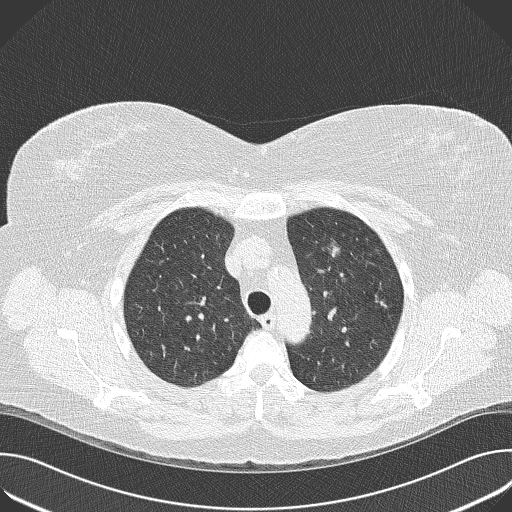
Low-dose screening chest CT, axial slice, baseline annual screen, lung window (W 1500 / L -600 HU), 120 kVp, slice 111 of 143 in the series, 512 × 512 image matrix. Female, age 57 years at enrolment.
Lesion marked by an expert reader, bounding box [x1, y1, x2, y2] px = [313, 233, 352, 270]. The screening reader recorded 3 non-calcified nodules or masses ≥4 mm on this exam; which of them this box marks is not recorded. Official screen result: positive, change unspecified: nodule(s) >= 4 mm or enlarging nodule(s), mass(es), or other non-specific abnormalities suspicious for lung cancer. Participant outcome: lung cancer diagnosed 446 days after this screen — adenocarcinoma, NOS, left upper lobe, poorly differentiated (G3), stage IA (AJCC 6th edition), 24 mm at pathology.